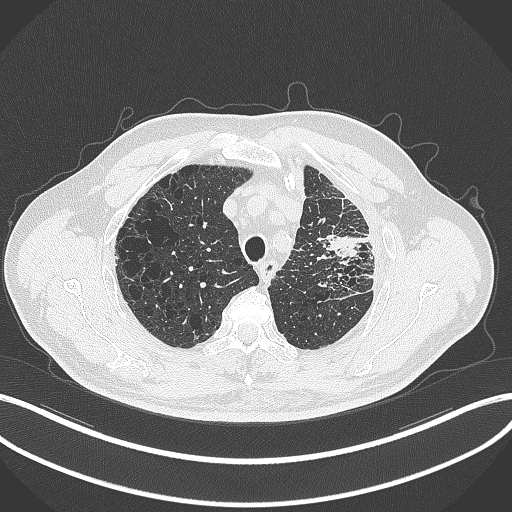
Chest CT, one axial slice; slice 260 of 297 in the series (ordered by position); reconstruction kernel B70f; lung window (W 1500 / L -600 HU); 1 mm slice thickness; 512 × 512 image matrix. Male patient, age 68 years. From the clinical record (not read from this slice): clinical TNM (as recorded): T3 N3 M1.
Annotated regions visible in this slice (rectangle marked by the reading radiologist):
- lung tumour (recorded histology: adenocarcinoma): bounding box <323,231,362,265> (left, top, right, bottom; pixels)